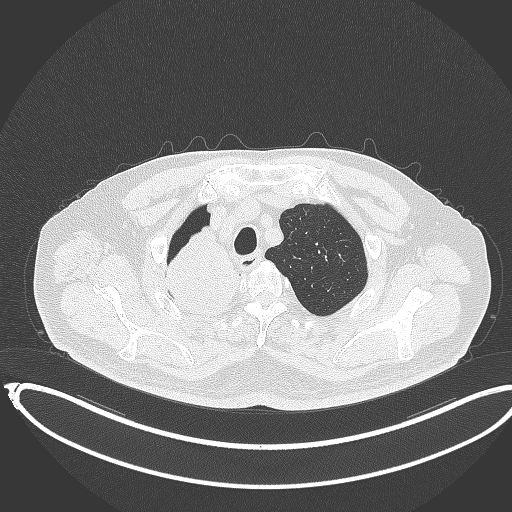
Chest CT, one axial slice; slice 315 of 403 in the series (ordered by position); reconstruction kernel B70f; 120 kVp; lung window (W 1500 / L -600 HU); 1 mm slice thickness; 512 × 512 image matrix, field of view 436 × 436 mm. Patient: male, 68 years. From the clinical record (not read from this slice): clinical TNM (as recorded): T2a N0 M0.
Structures marked on this image (bounding box drawn by a radiologist):
- lung tumour (recorded histology: adenocarcinoma): bounding box (x1, y1, x2, y2) in pixels: (157, 227, 248, 323)